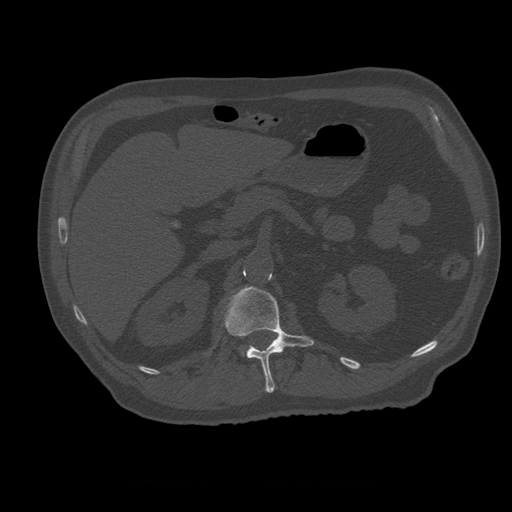
CT including the spine, one axial slice; reconstruction kernel STANDARD; bone window (W 1800 / L 400 HU); 512 × 512 image matrix, field of view 407 × 407 mm. Patient age 73 years. Case-level facts recorded for this patient, not image findings: primary cancer: prostate; vertebrae with lytic lesions (as recorded): L2.
Structures marked on this image (semi-automatic segmentation, software-assisted and operator-edited):
- L1 vertebra: bounding box (x1, y1, x2, y2) in pixels: (224, 287, 314, 393)